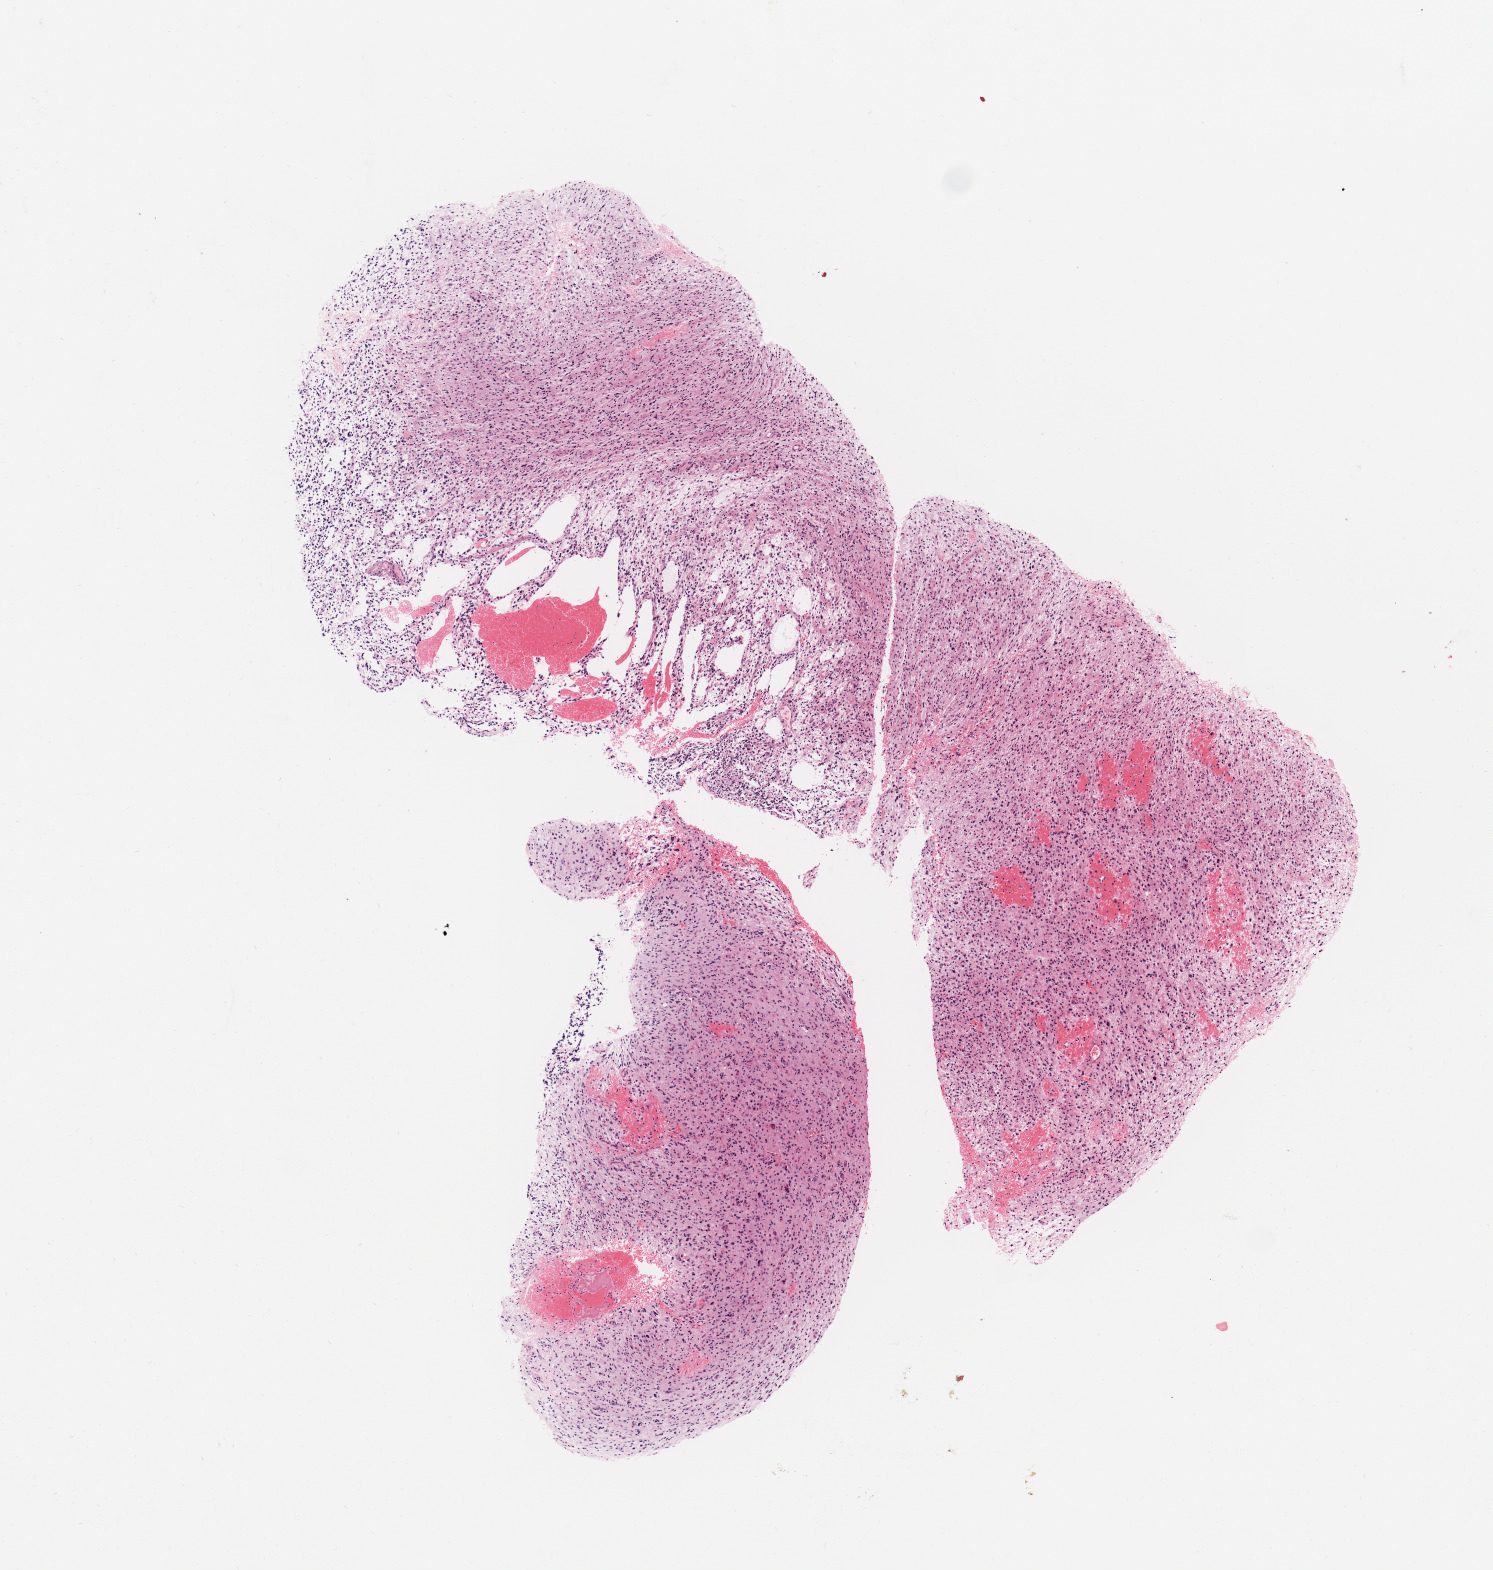
Whole-slide histology image, H&E, a low-resolution overview of the entire scanned area, about 5.9 x 6.2 mm, brain, tumour tissue. Female, 65 y/o.
- diagnosis: Glioblastoma